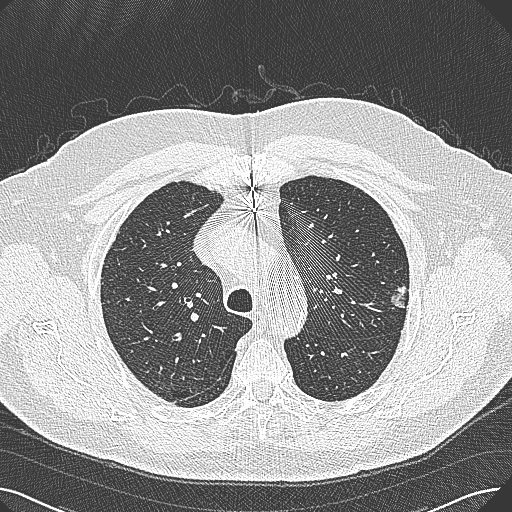
Low-dose screening chest CT, axial slice; baseline screening round; lung window (W 1500 / L -600 HU); 1 mm slice thickness; slice 73 of 269 in the series. Male, age 74 years at enrolment.
• Expert reader's lesion annotation, bounding box (x1, y1, x2, y2) in pixels: (377, 273, 423, 316).
• Reader record for this screening exam (exam-level; its link to the box is not recorded): non-calcified nodule or mass ≥4 mm, left upper lobe, 15 × 10 mm, poorly defined margins, soft tissue attenuation.